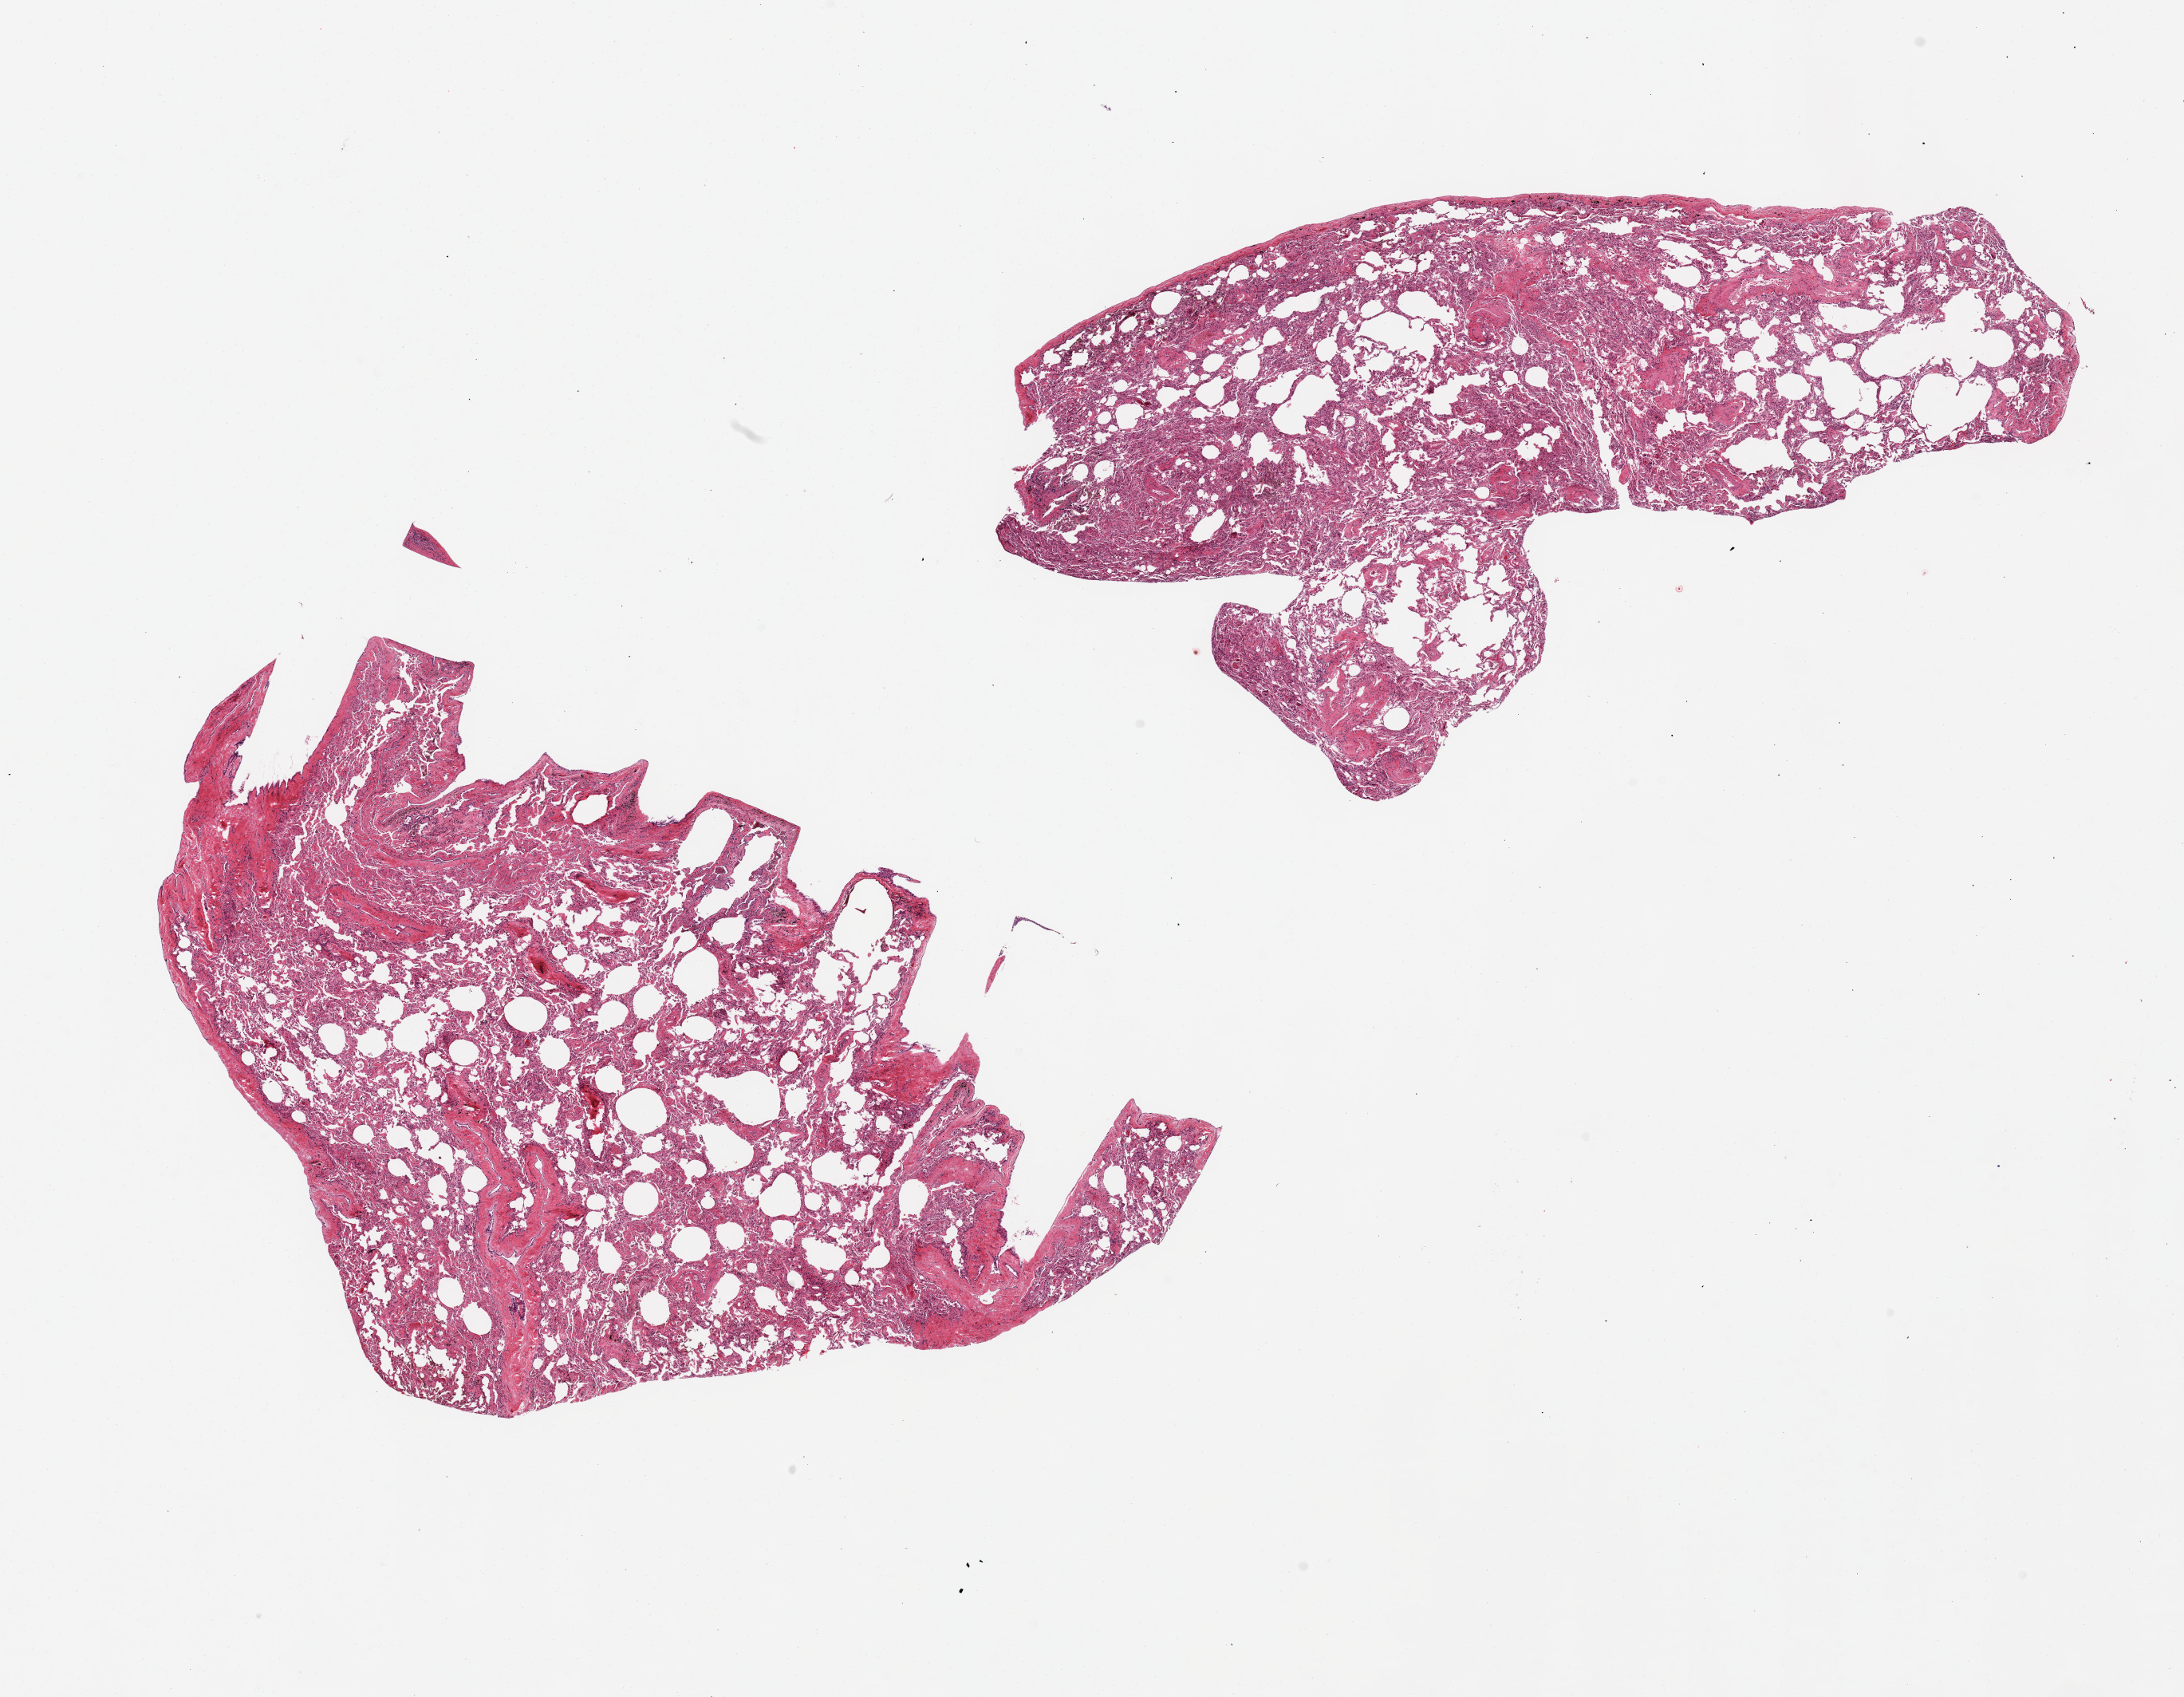
Digitized haematoxylin and eosin-stained section — a low-resolution overview of the entire scanned area, about 21.7 x 16.8 mm; PAXgene-fixed paraffin-embedded (PFPE) section; sampled site (target tissue): lung; donor tissue sample. Donor sex: female.
Pathologist's review note for this sample: 2 pieces 10x6 mm; patchy emphysema.